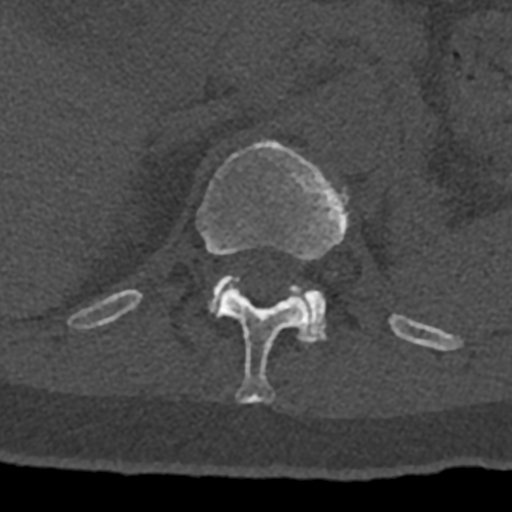
CT including the spine, one axial slice; position 478 of 797 along the scan axis; 120 kVp; bone window (W 1800 / L 400 HU); 0.5 mm slice thickness; 512 × 512 image matrix, field of view 160 × 160 mm. Patient: male, 74 years. From the clinical record (not read from this slice): primary cancer: renal; vertebrae with lytic lesions (as recorded): T10, L1, L2, L3, L4, L5.
Structures marked on this image (semi-automatic segmentation, software-assisted and operator-edited):
- L1 vertebra: bounding box (x1, y1, x2, y2) in pixels: (208, 275, 328, 343)
- T12 vertebra: (70, 140, 432, 404)